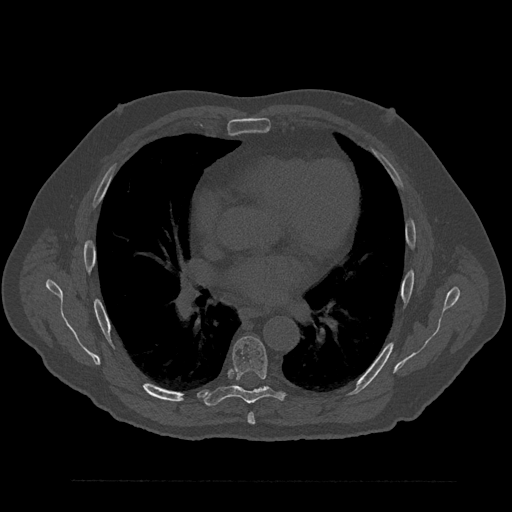
CT including the spine, one axial slice; slice 510 of 797 in the series (ordered by position); reconstruction kernel Br40s/3; bone window (W 1800 / L 400 HU); 0.5 mm slice thickness; 512 × 512 image matrix, field of view 430 × 430 mm. Patient: male, 61 years. Case-level facts recorded for this patient, not image findings: primary cancer: prostate.
Outlined on this slice (semi-automatically segmented with operator editing):
- T6 vertebra: bounding box (x1, y1, x2, y2) in pixels: (247, 412, 255, 425)
- T7 vertebra: (204, 336, 284, 406)